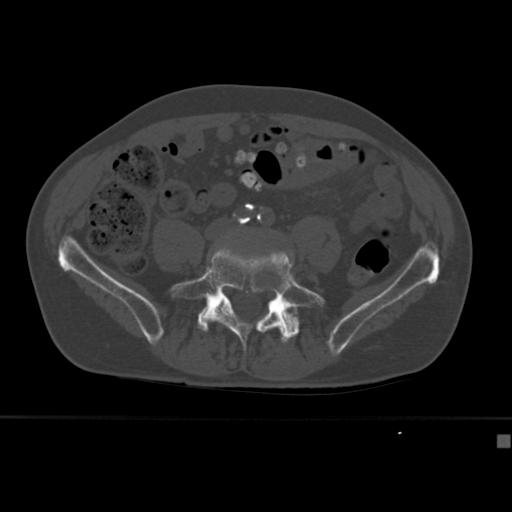
CT including the spine, one axial slice. Slice 88 of 430 in the series (ordered by position). 120 kVp. Bone window (W 1800 / L 400 HU). 1.5 mm slice thickness. 512 × 512 image matrix. Male patient, age 64 years. Case-level facts recorded for this patient, not image findings: primary cancer: uterus.
Structures marked on this image (semi-automatic segmentation, software-assisted and operator-edited):
- L5 vertebra: bounding box [x1, y1, x2, y2] px = [170, 246, 326, 353]